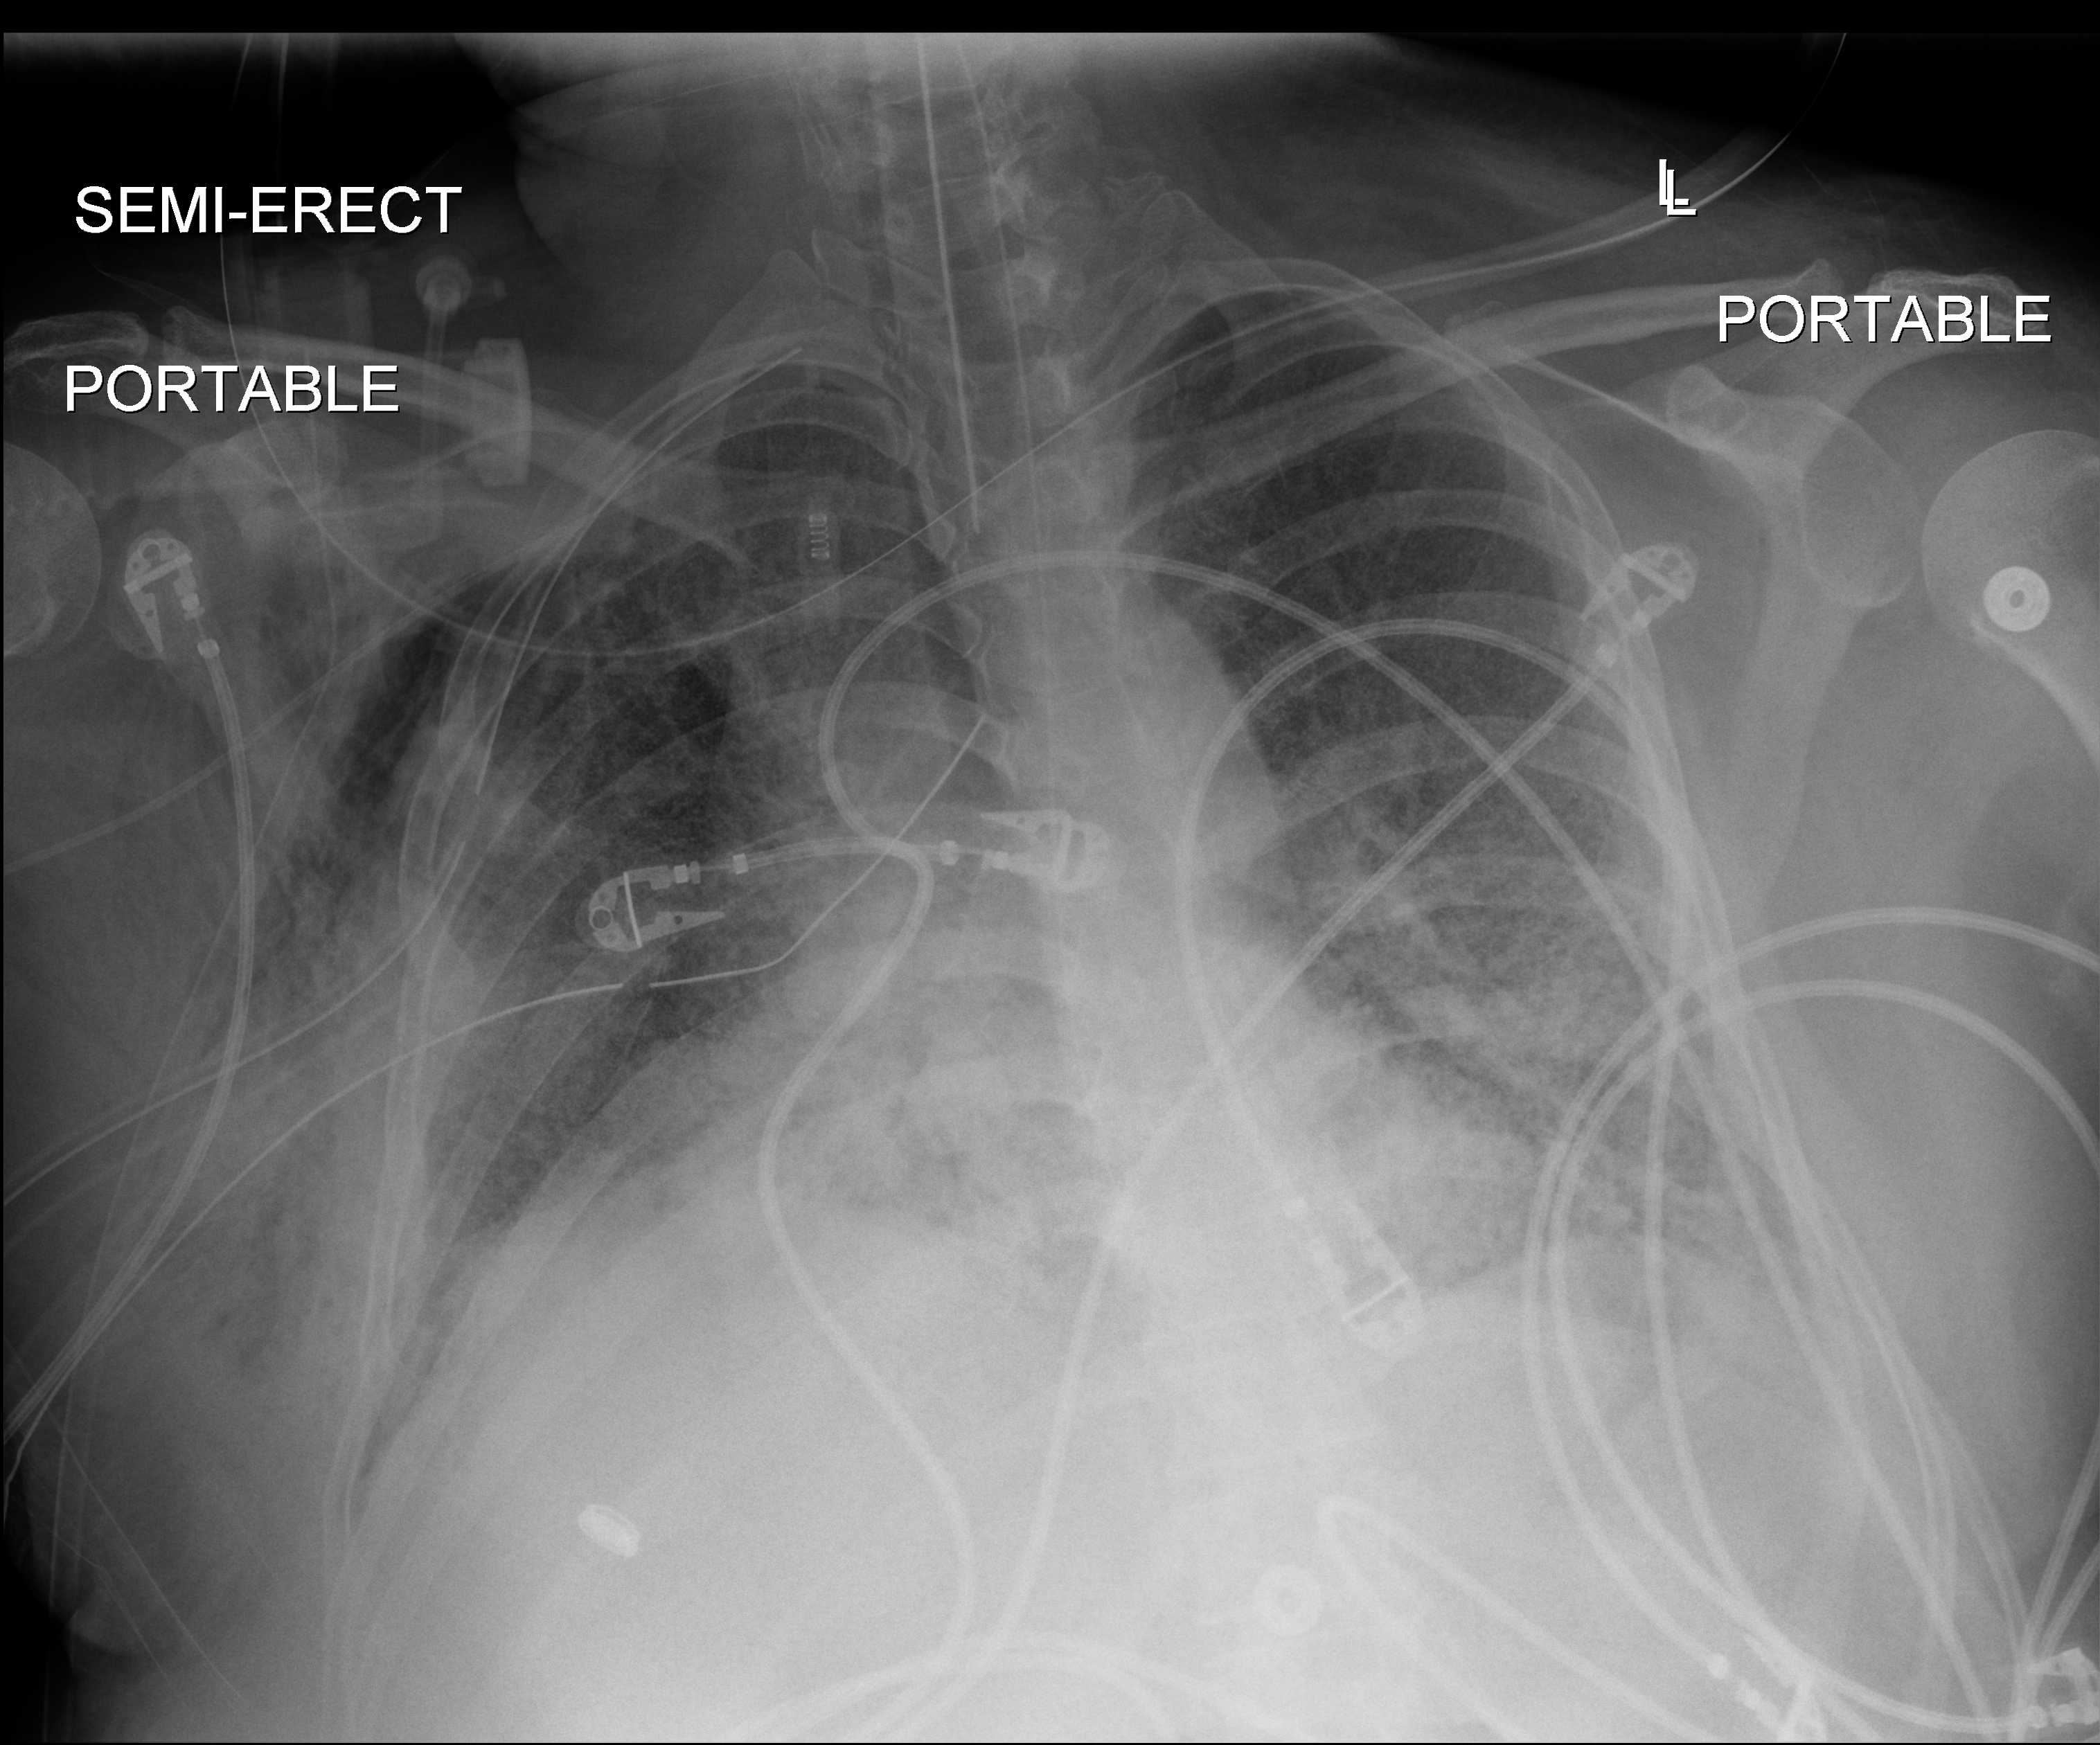
Chest X-ray (portable), anteroposterior (AP) projection. Patient hospitalised with COVID-19, aged 18–59 years.
Admission-level facts for this patient (not findings on this image; timing relative to this image not recorded): smoking status (admission record): never.